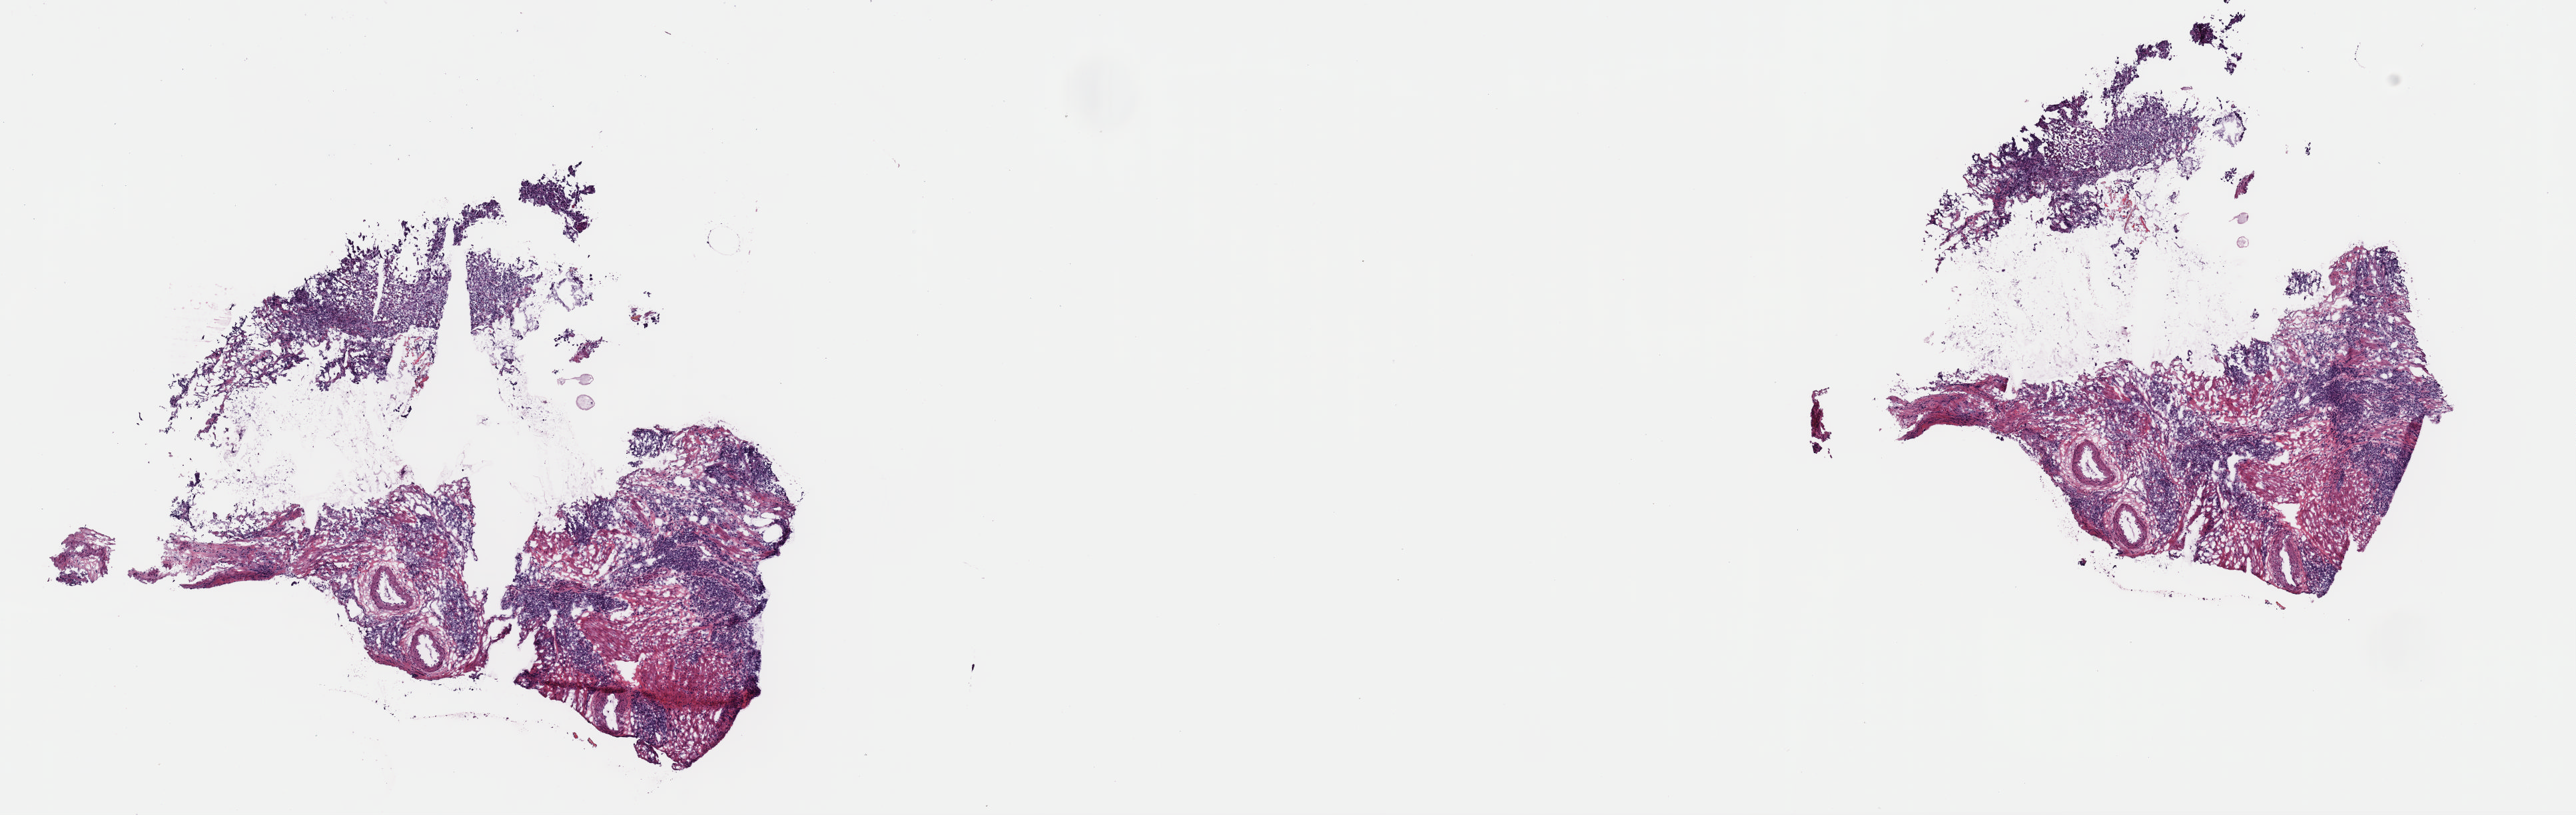
Whole-slide histology image, Hematoxylin and eosin (H&E) stained, whole scanned area (about 15.3 x 4.8 mm) shown as a low-resolution overview, frozen section from the top of the tissue portion, sample: primary tumour, cervix. Female patient; age at initial diagnosis 45 years. Histologic grade: G3 (poorly differentiated). Pathologist review of this section (percent, as recorded): tumour cells 100%, tumour nuclei 80%, normal cells 0%, stromal cells 0%, necrosis 0%. Infiltration values recorded for this section: lymphocyte infiltration 2%, monocyte infiltration 0%, neutrophil infiltration 0%.
Histologic diagnosis: Squamous cell carcinoma, NOS (cervix uteri). FIGO stage: IB1. Lymph nodes positive (case pathology): 0 of 2 examined.